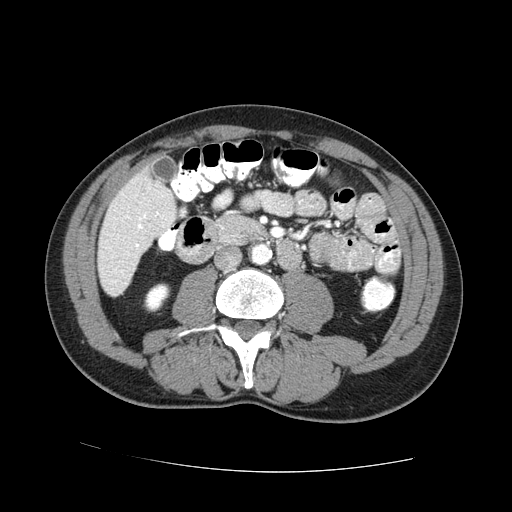
Contrast-enhanced abdominal CT (liver protocol), one axial slice. Slice 14 of 73 in the series (ordered by position). Reconstruction kernel STANDARD. 100 kVp. One of 2 acquisitions stored at this slice position. Soft-tissue window (W 400 / L 40 HU). 512 × 512 image matrix, field of view 380 × 380 mm. From the clinical record (not read from this slice): diagnosis: hepatocellular carcinoma (patient treated with transarterial chemoembolisation; whether this scan precedes or follows treatment is not stated here); TNM stage (as recorded): Stage-IVA; Child-Pugh class: A.
Structures marked on this image (semi-automatic segmentation, software-assisted and operator-edited):
- liver parenchyma outside the tumour (the mass and vessels are separate outlines, so this box may not span the whole liver): bounding box <98,165,176,296> (left, top, right, bottom; pixels)
- liver vessels: <127,213,158,247>